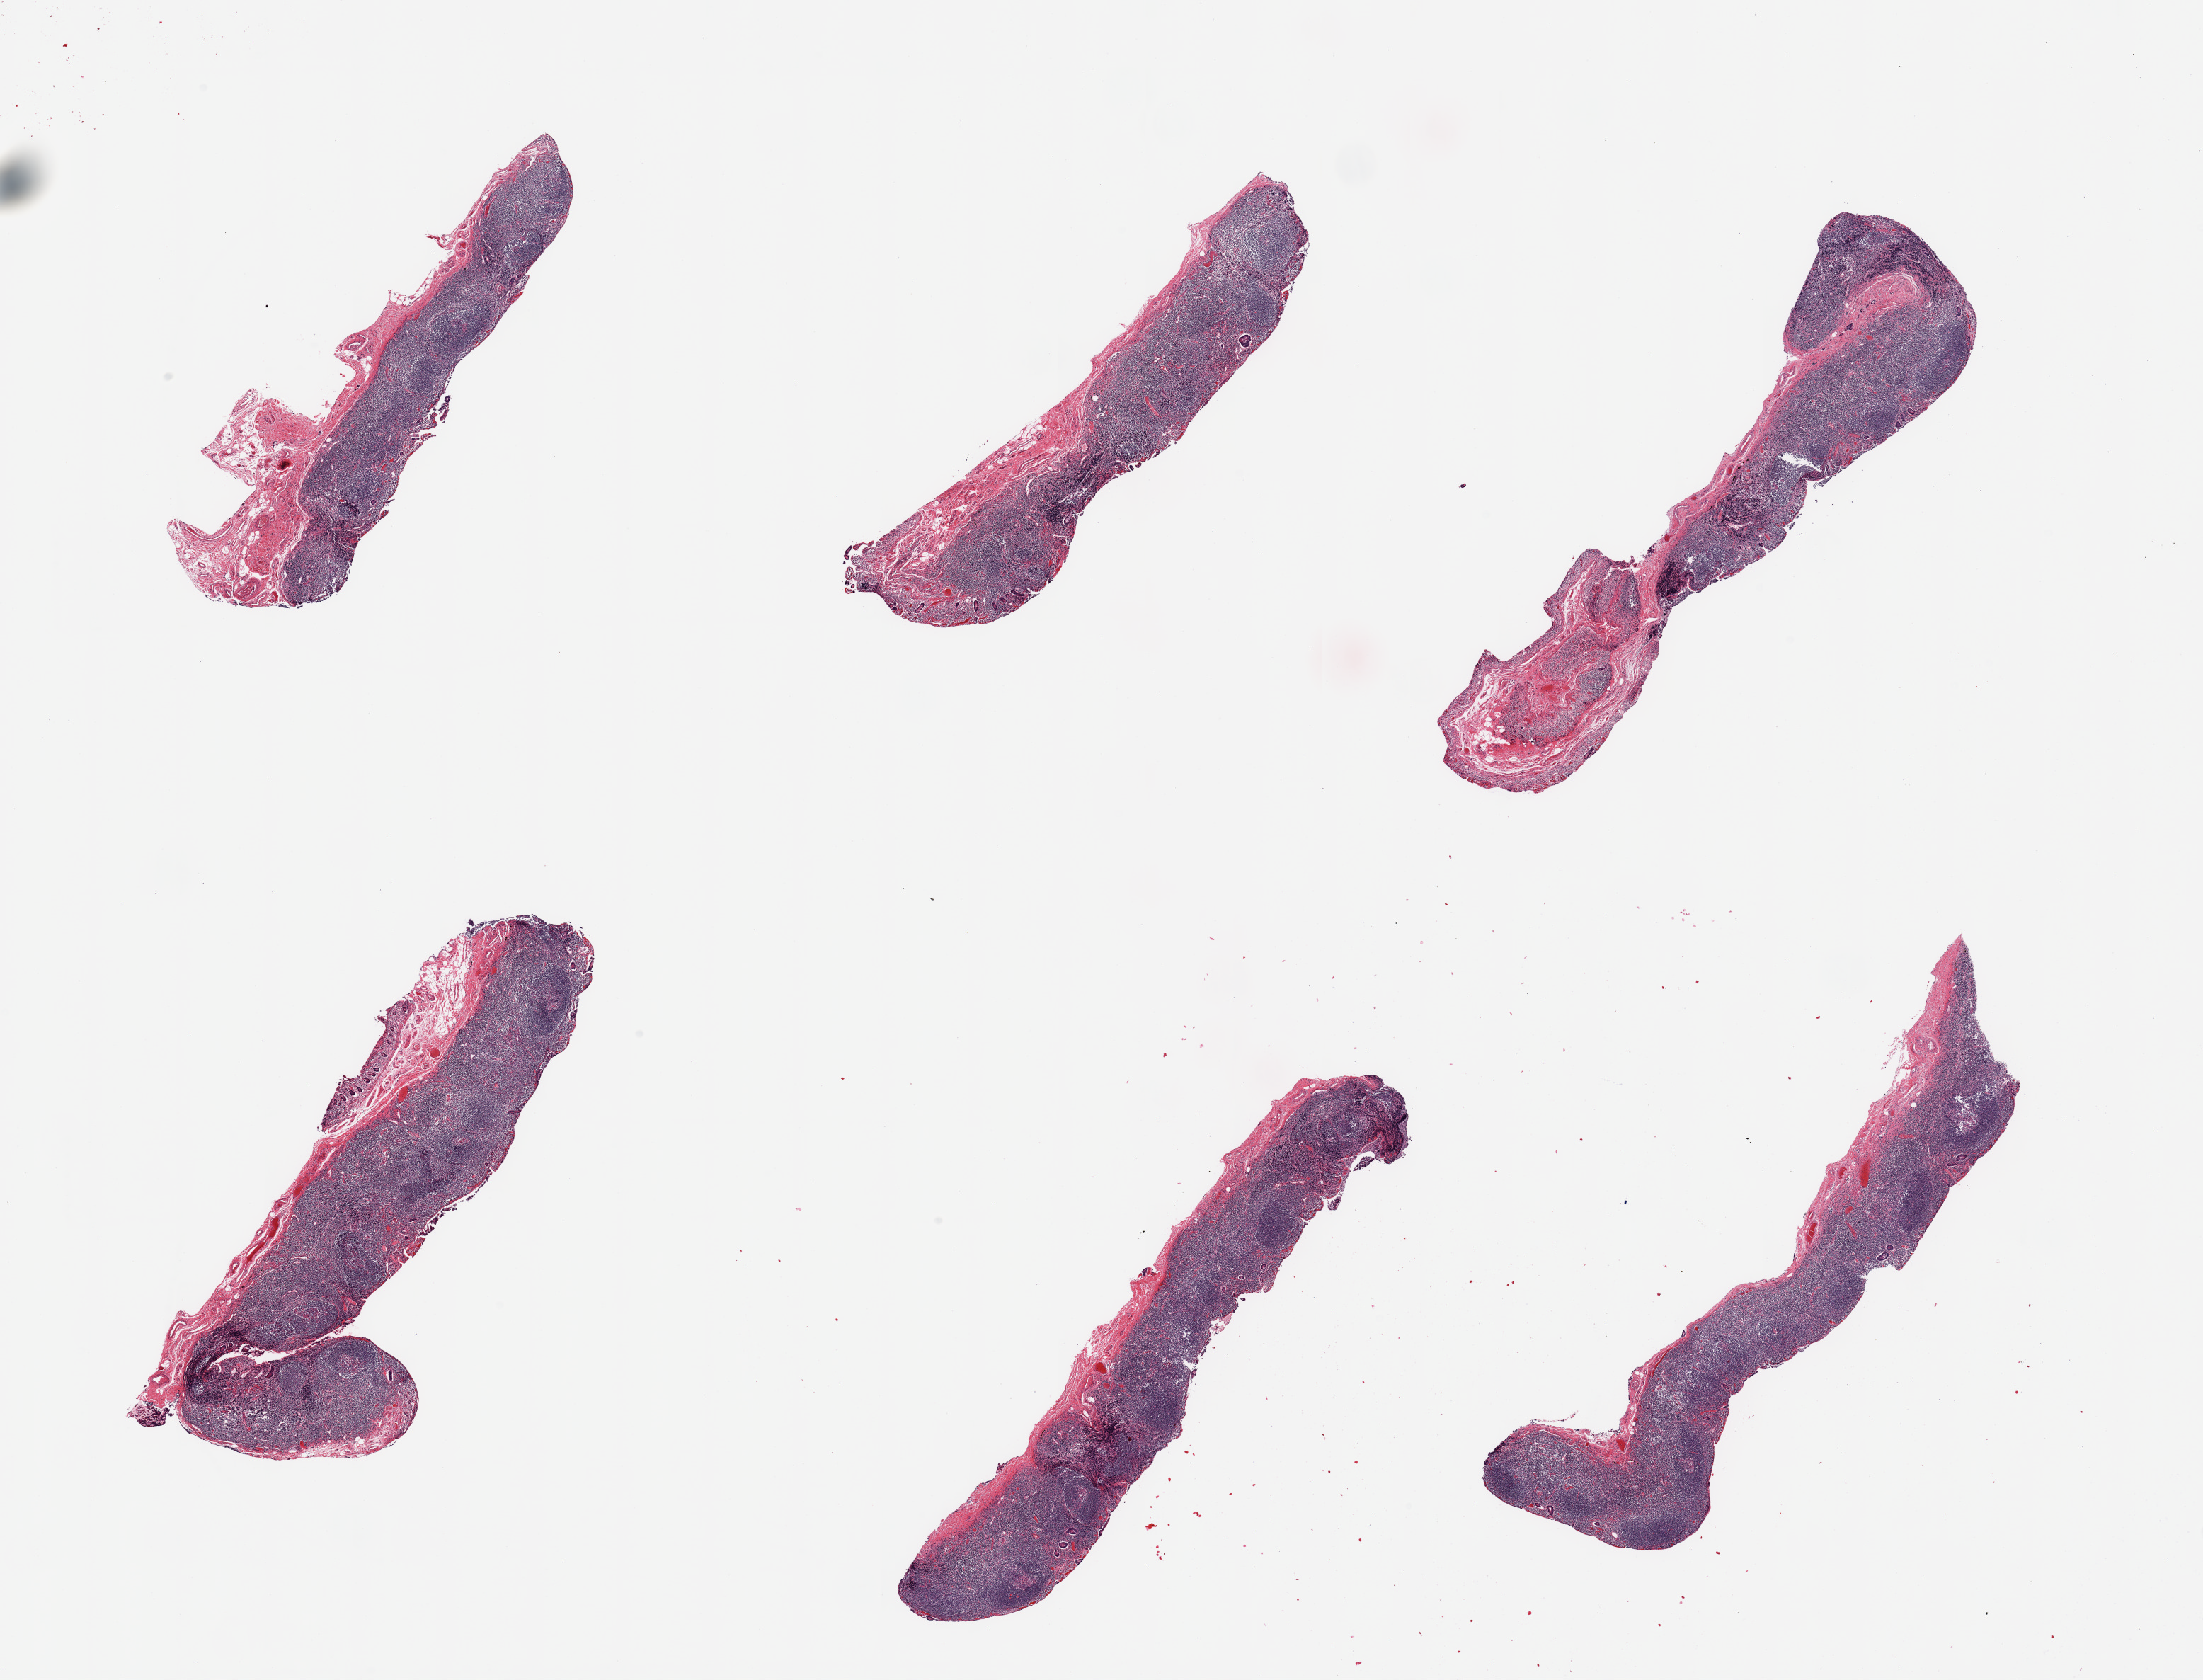
Digitized hematoxylin and eosin (H&E)-stained section, a low-resolution overview of the entire scanned area, about 24.6 x 18.8 mm (from a 20x scan), PAXgene-fixed paraffin-embedded (PFPE) section, sampled site (target tissue): ileum, tissue donor sample. Male donor.
Review note (as recorded): 6 pieces; lymphoid infiltrate with numerous well defined follicles and reactive germinal centers c/w florid follicular hyperplasia.